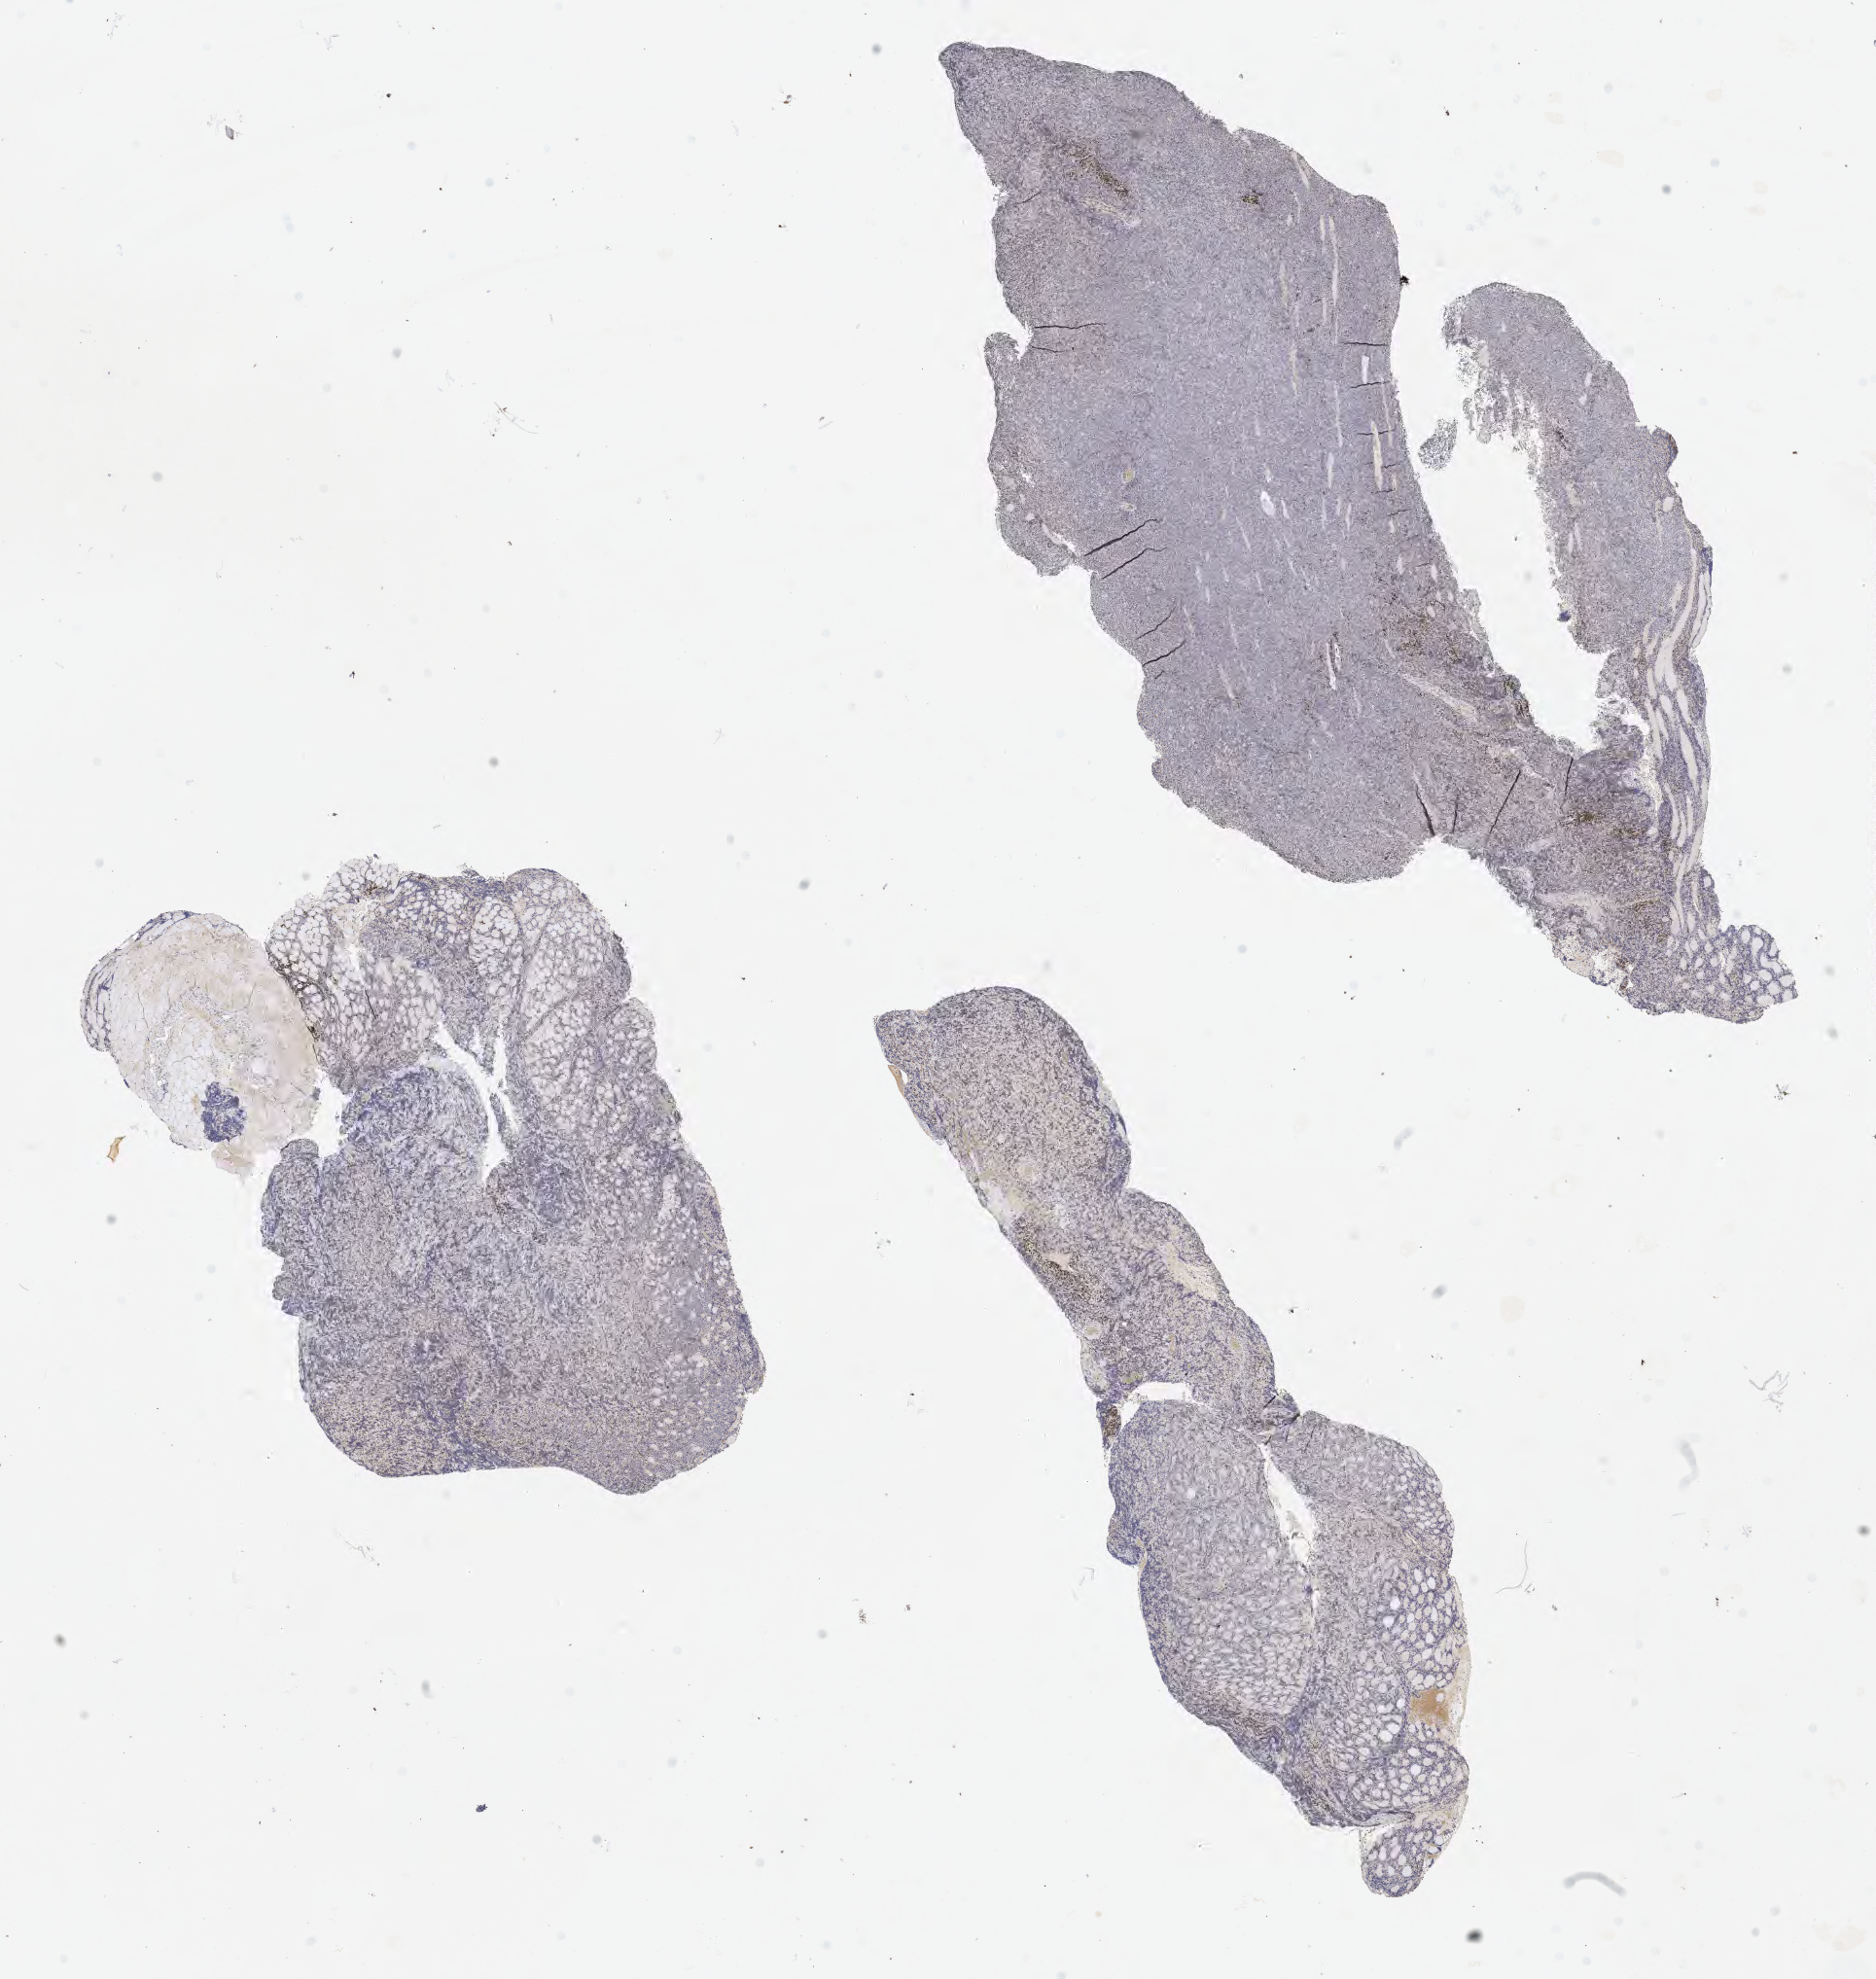
IHC for BCL2, whole-slide image — low-resolution overview of the scanned area, about 15.6 x 16.5 mm; tumor tissue; site: lymph node of head and neck. Male patient, aged 55.
Histologic diagnosis: Burkitt lymphoma, NOS.